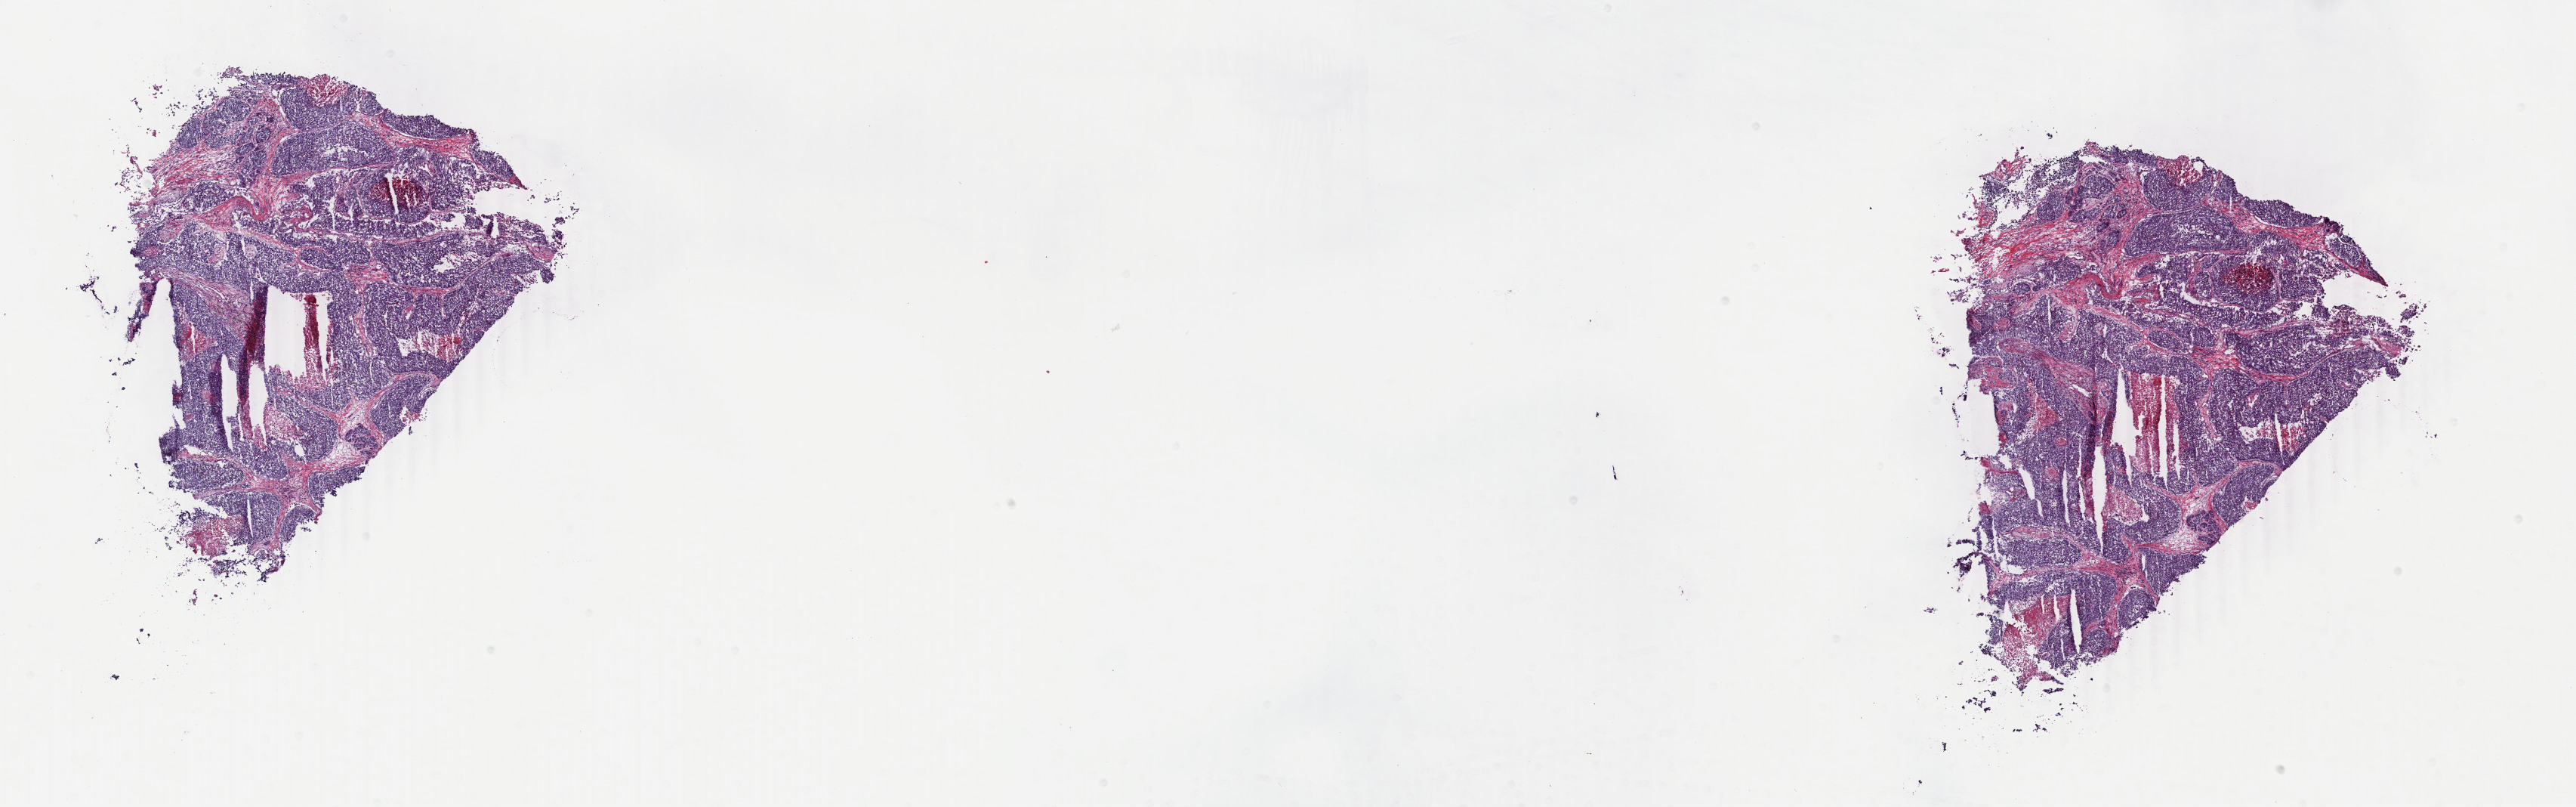
H&E-stained whole-slide image, shown as a low-resolution overview of the whole scanned area (about 27.1 x 8.5 mm), frozen section, breast, primary tumour sample. Female patient; age at initial diagnosis 59 years. Composition of this section per pathologist review: tumour cells 90%, tumour nuclei 95%, normal cells 0%, stromal cells 0%, necrosis 10%. Inflammatory infiltration, as recorded: lymphocyte infiltration 0%, monocyte infiltration 0%, neutrophil infiltration 0%.
Pathologic diagnosis: Infiltrating duct carcinoma, NOS. Lymph nodes positive (case pathology): 7 of 26 examined. AJCC pathologic stage: IIIA.